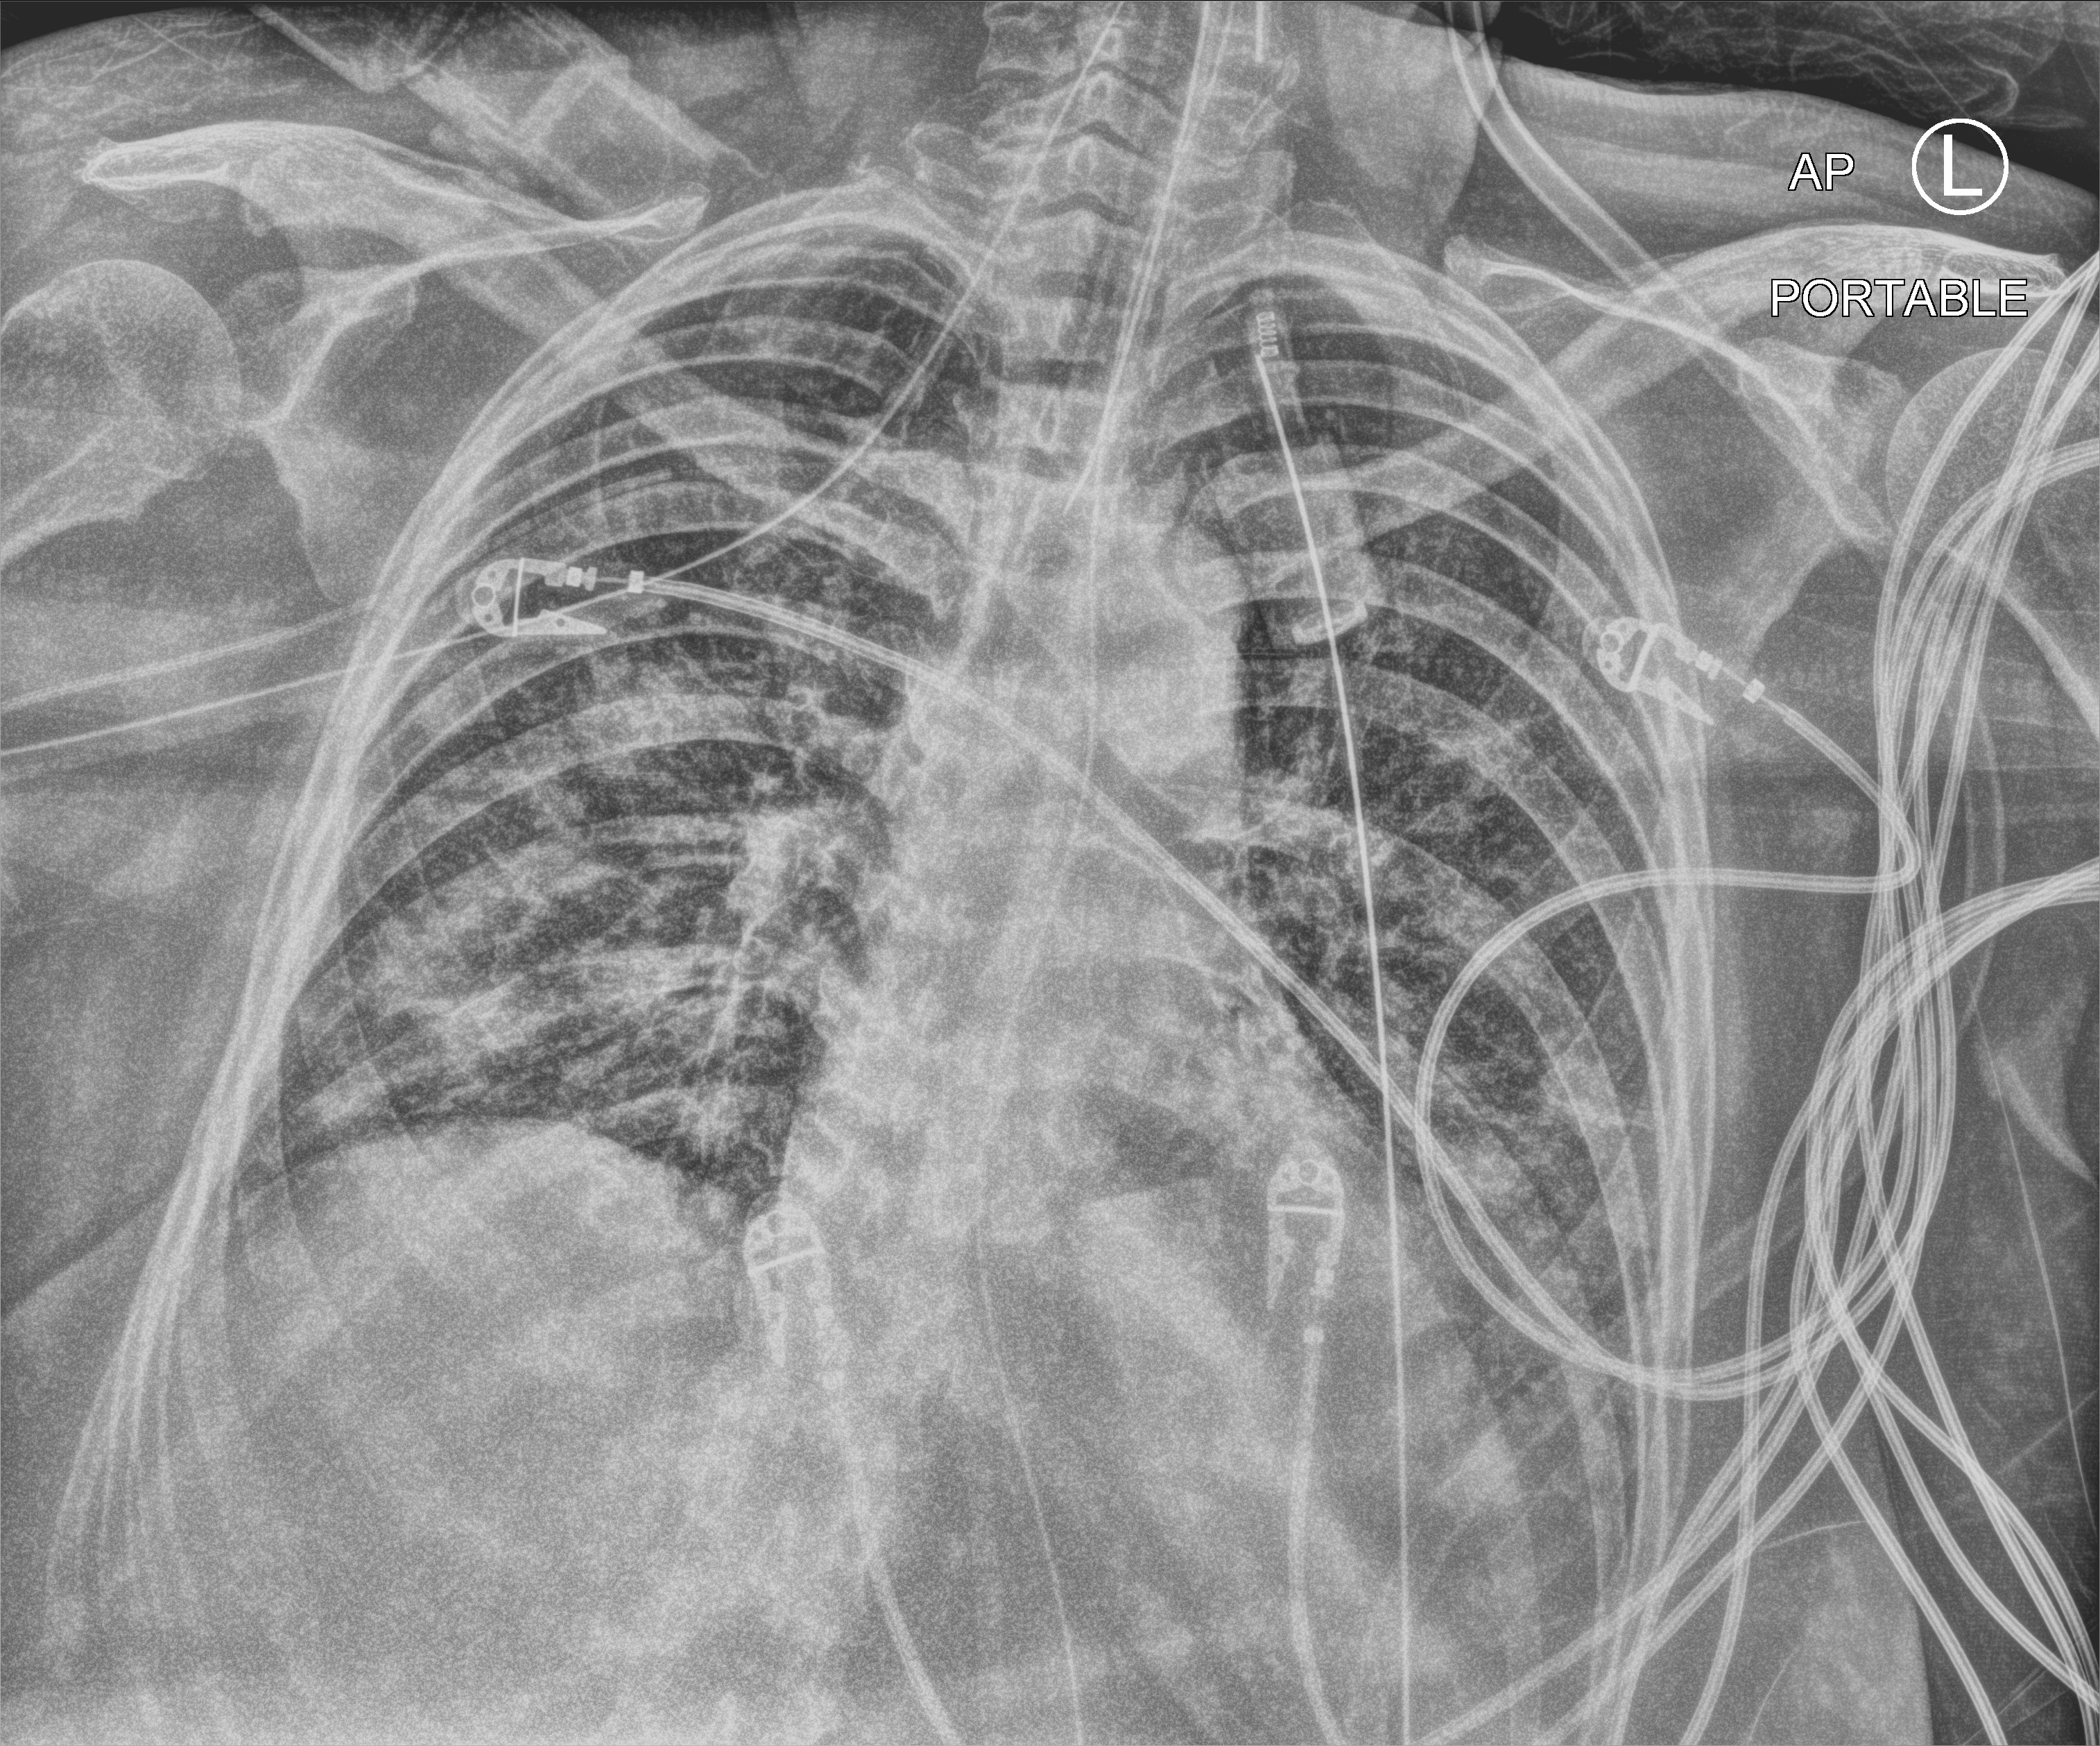
Bedside chest radiograph (computed radiography), anteroposterior (AP) projection. Patient hospitalised with COVID-19; female, aged 75–90 years.
Hospital-stay facts (about this admission, not read from this image; timing relative to this image not recorded): admitted to intensive care during this hospital stay: yes; mechanically ventilated during this hospital stay: yes.